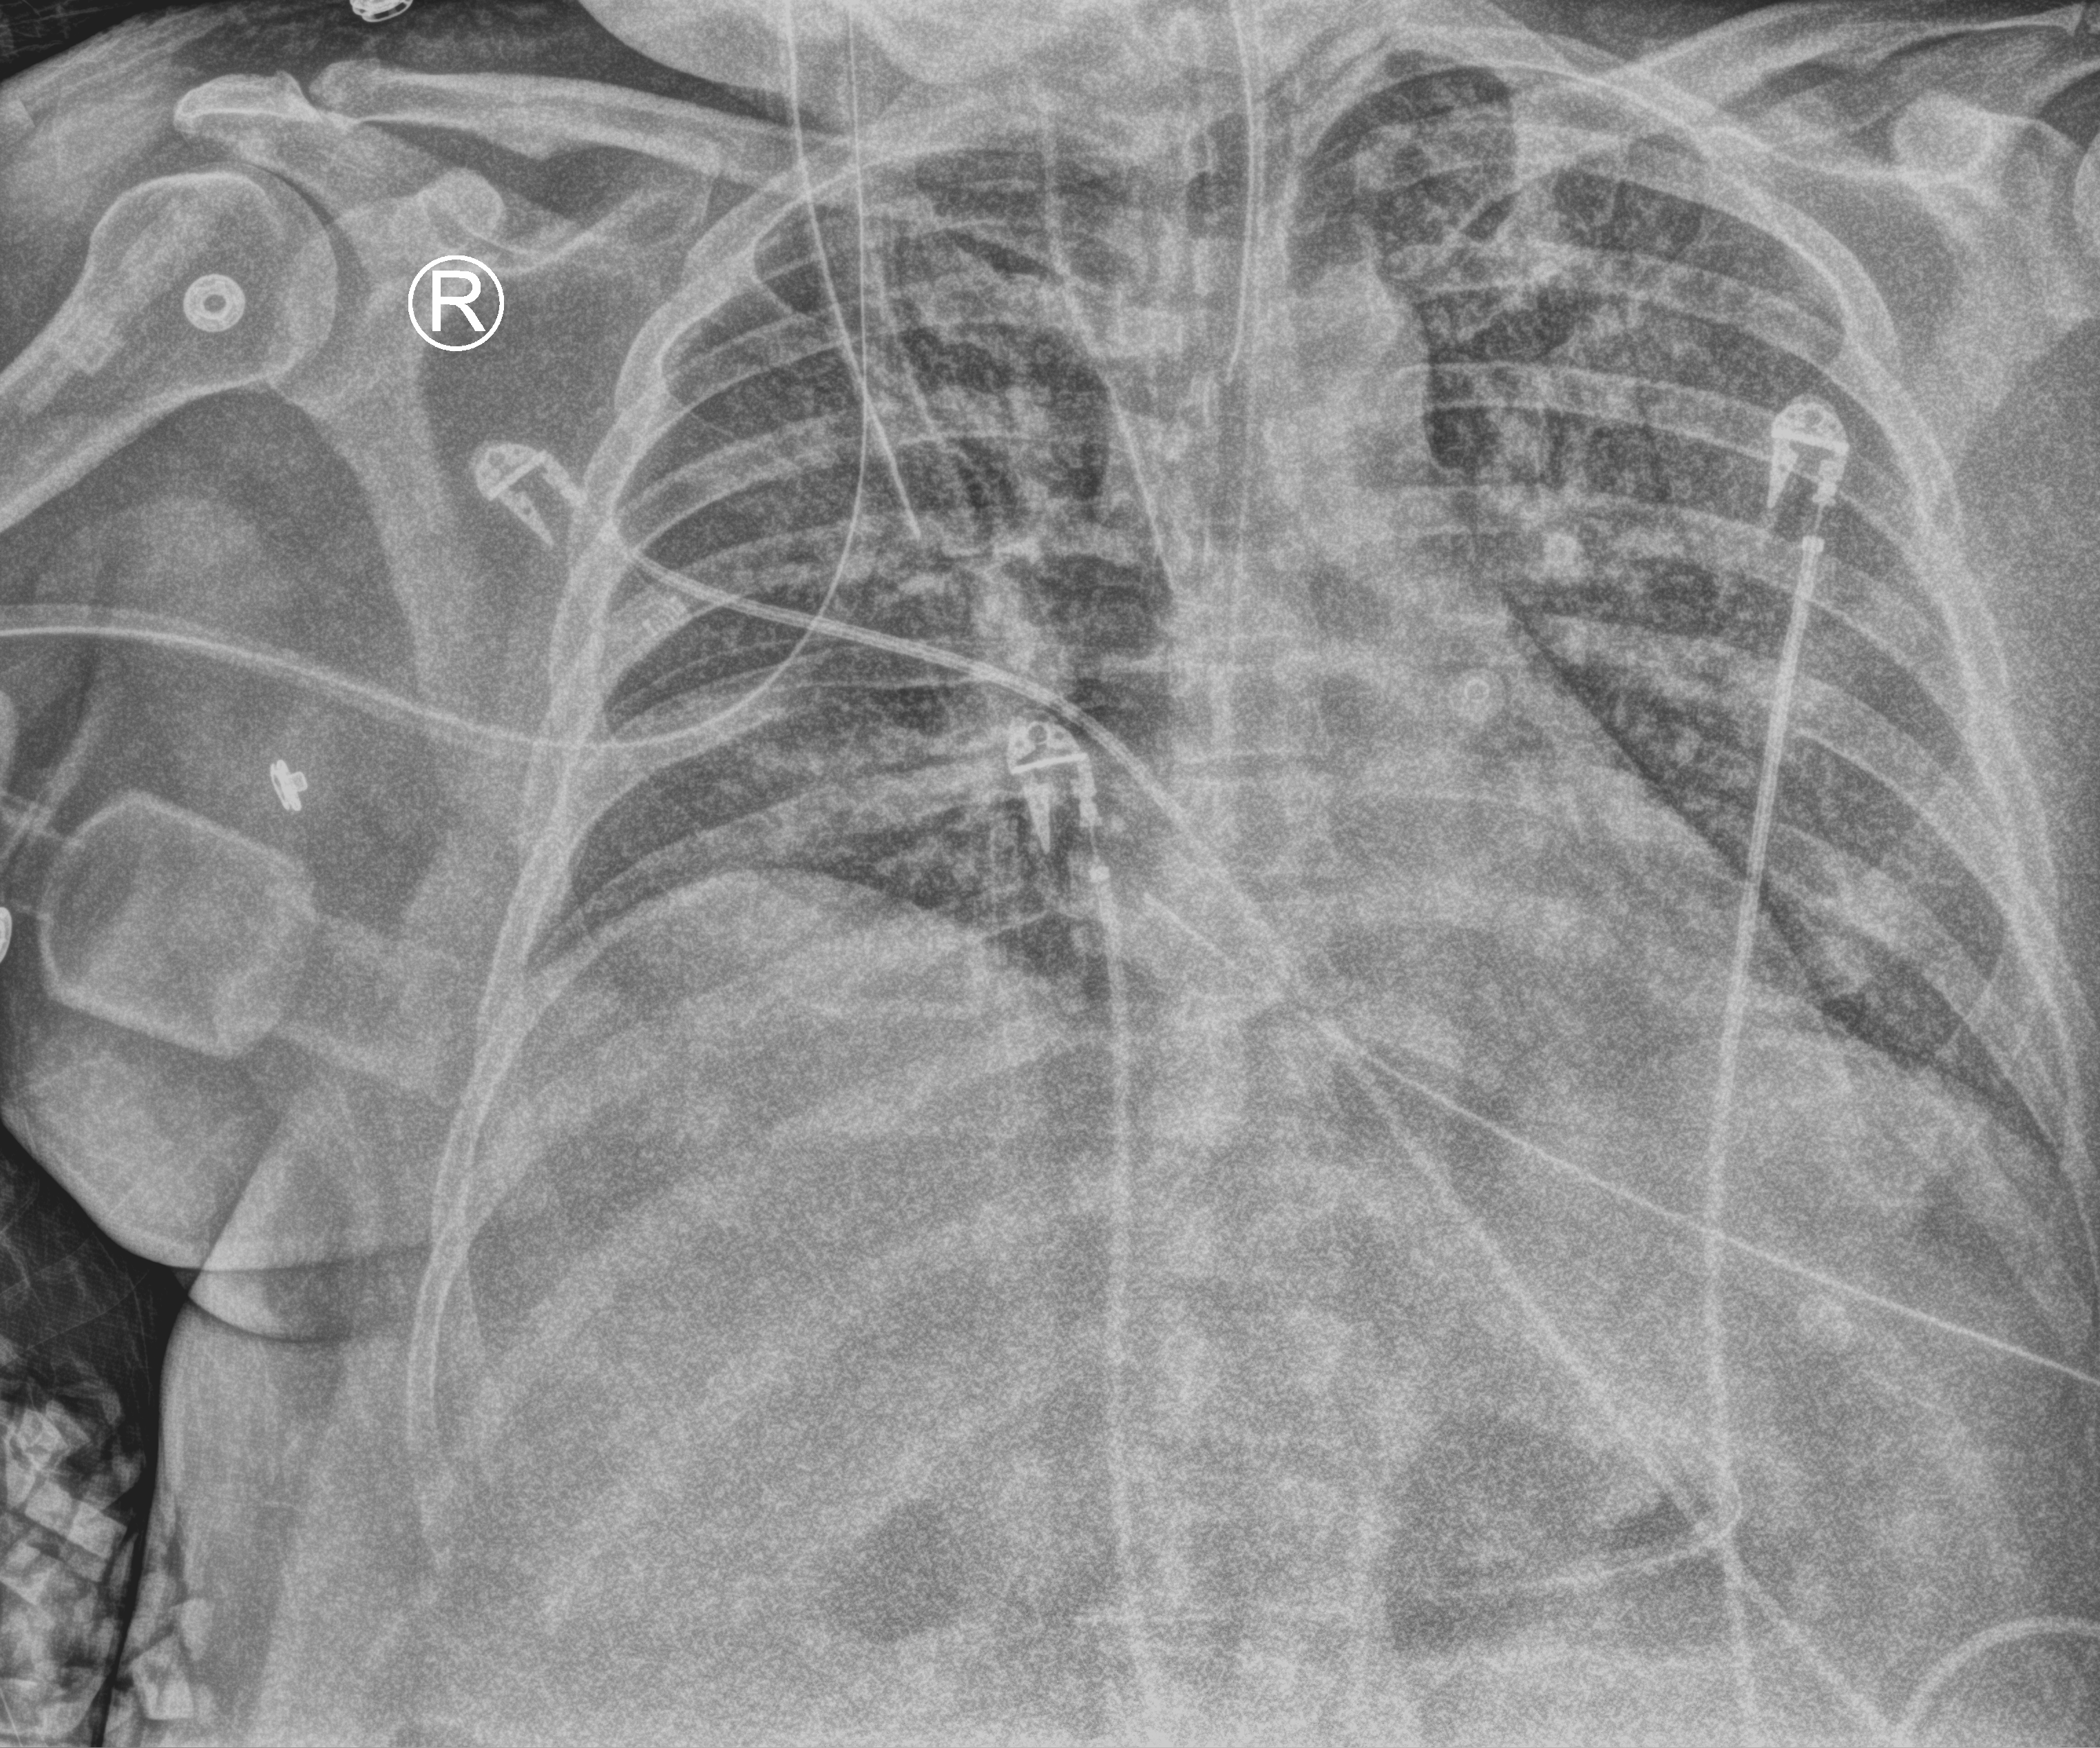
Chest X-ray (portable), anteroposterior (AP) projection. Male patient hospitalised with COVID-19, age 18–59 years.
Hospital-stay facts (about this admission, not read from this image; timing relative to this image not recorded): mechanically ventilated during this hospital stay: yes.